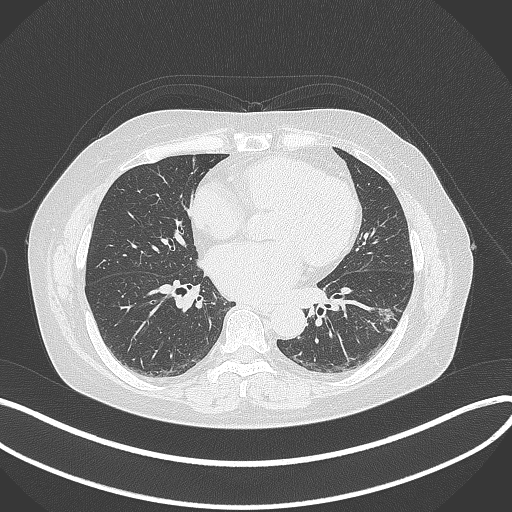
Chest CT, one axial slice. Slice 156 of 373 in the series (ordered by position). Reconstruction kernel B70f. 120 kVp. Lung window (W 1500 / L -600 HU). 512 × 512 image matrix. Female patient, age 67 years. From the clinical record (not read from this slice): clinical TNM (as recorded): T1c N0 M0.
Structures marked on this image (bounding box drawn by a radiologist):
- lung tumour (recorded histology: adenocarcinoma): bounding box (x1, y1, x2, y2) in pixels: (367, 300, 402, 334)